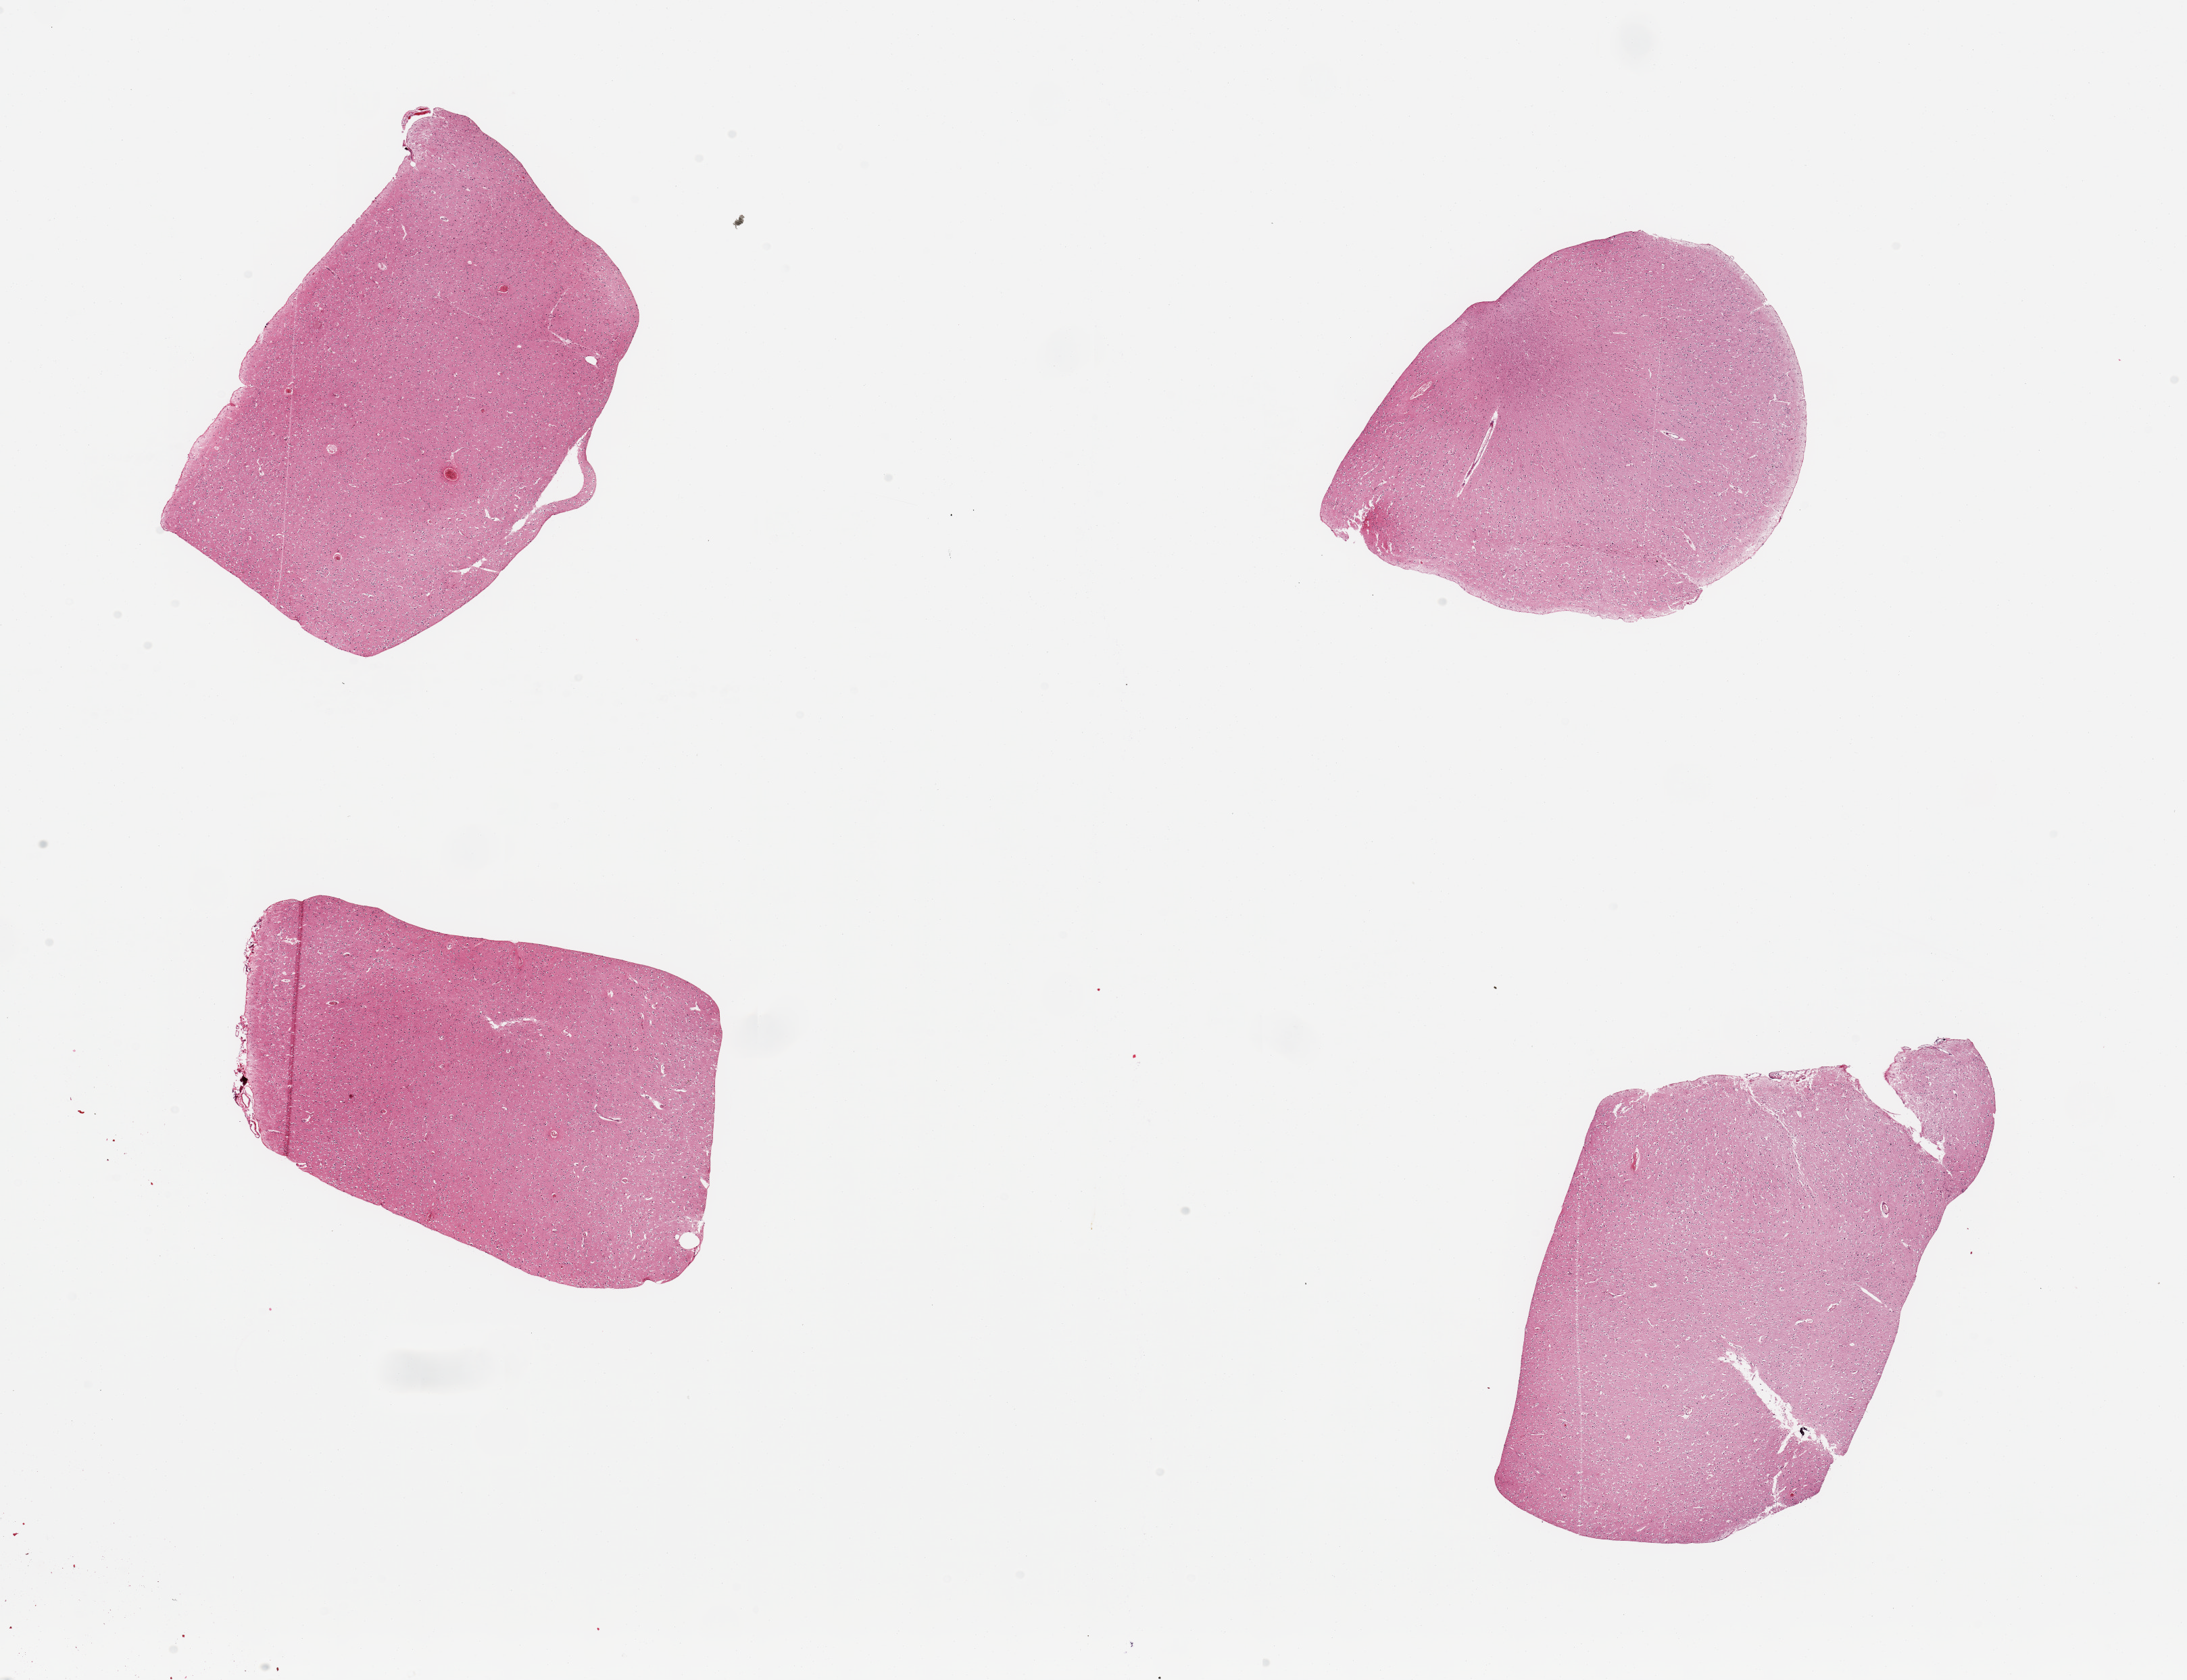
Whole-slide image, haematoxylin and eosin stain — whole scanned area (about 25.6 x 19.7 mm) shown as a low-resolution overview; PAXgene-fixed paraffin-embedded (PFPE) section; target tissue: cerebral cortex; tissue donor sample.
Reviewer comment on this tissue sample: 4 pieces, no abnormalities.